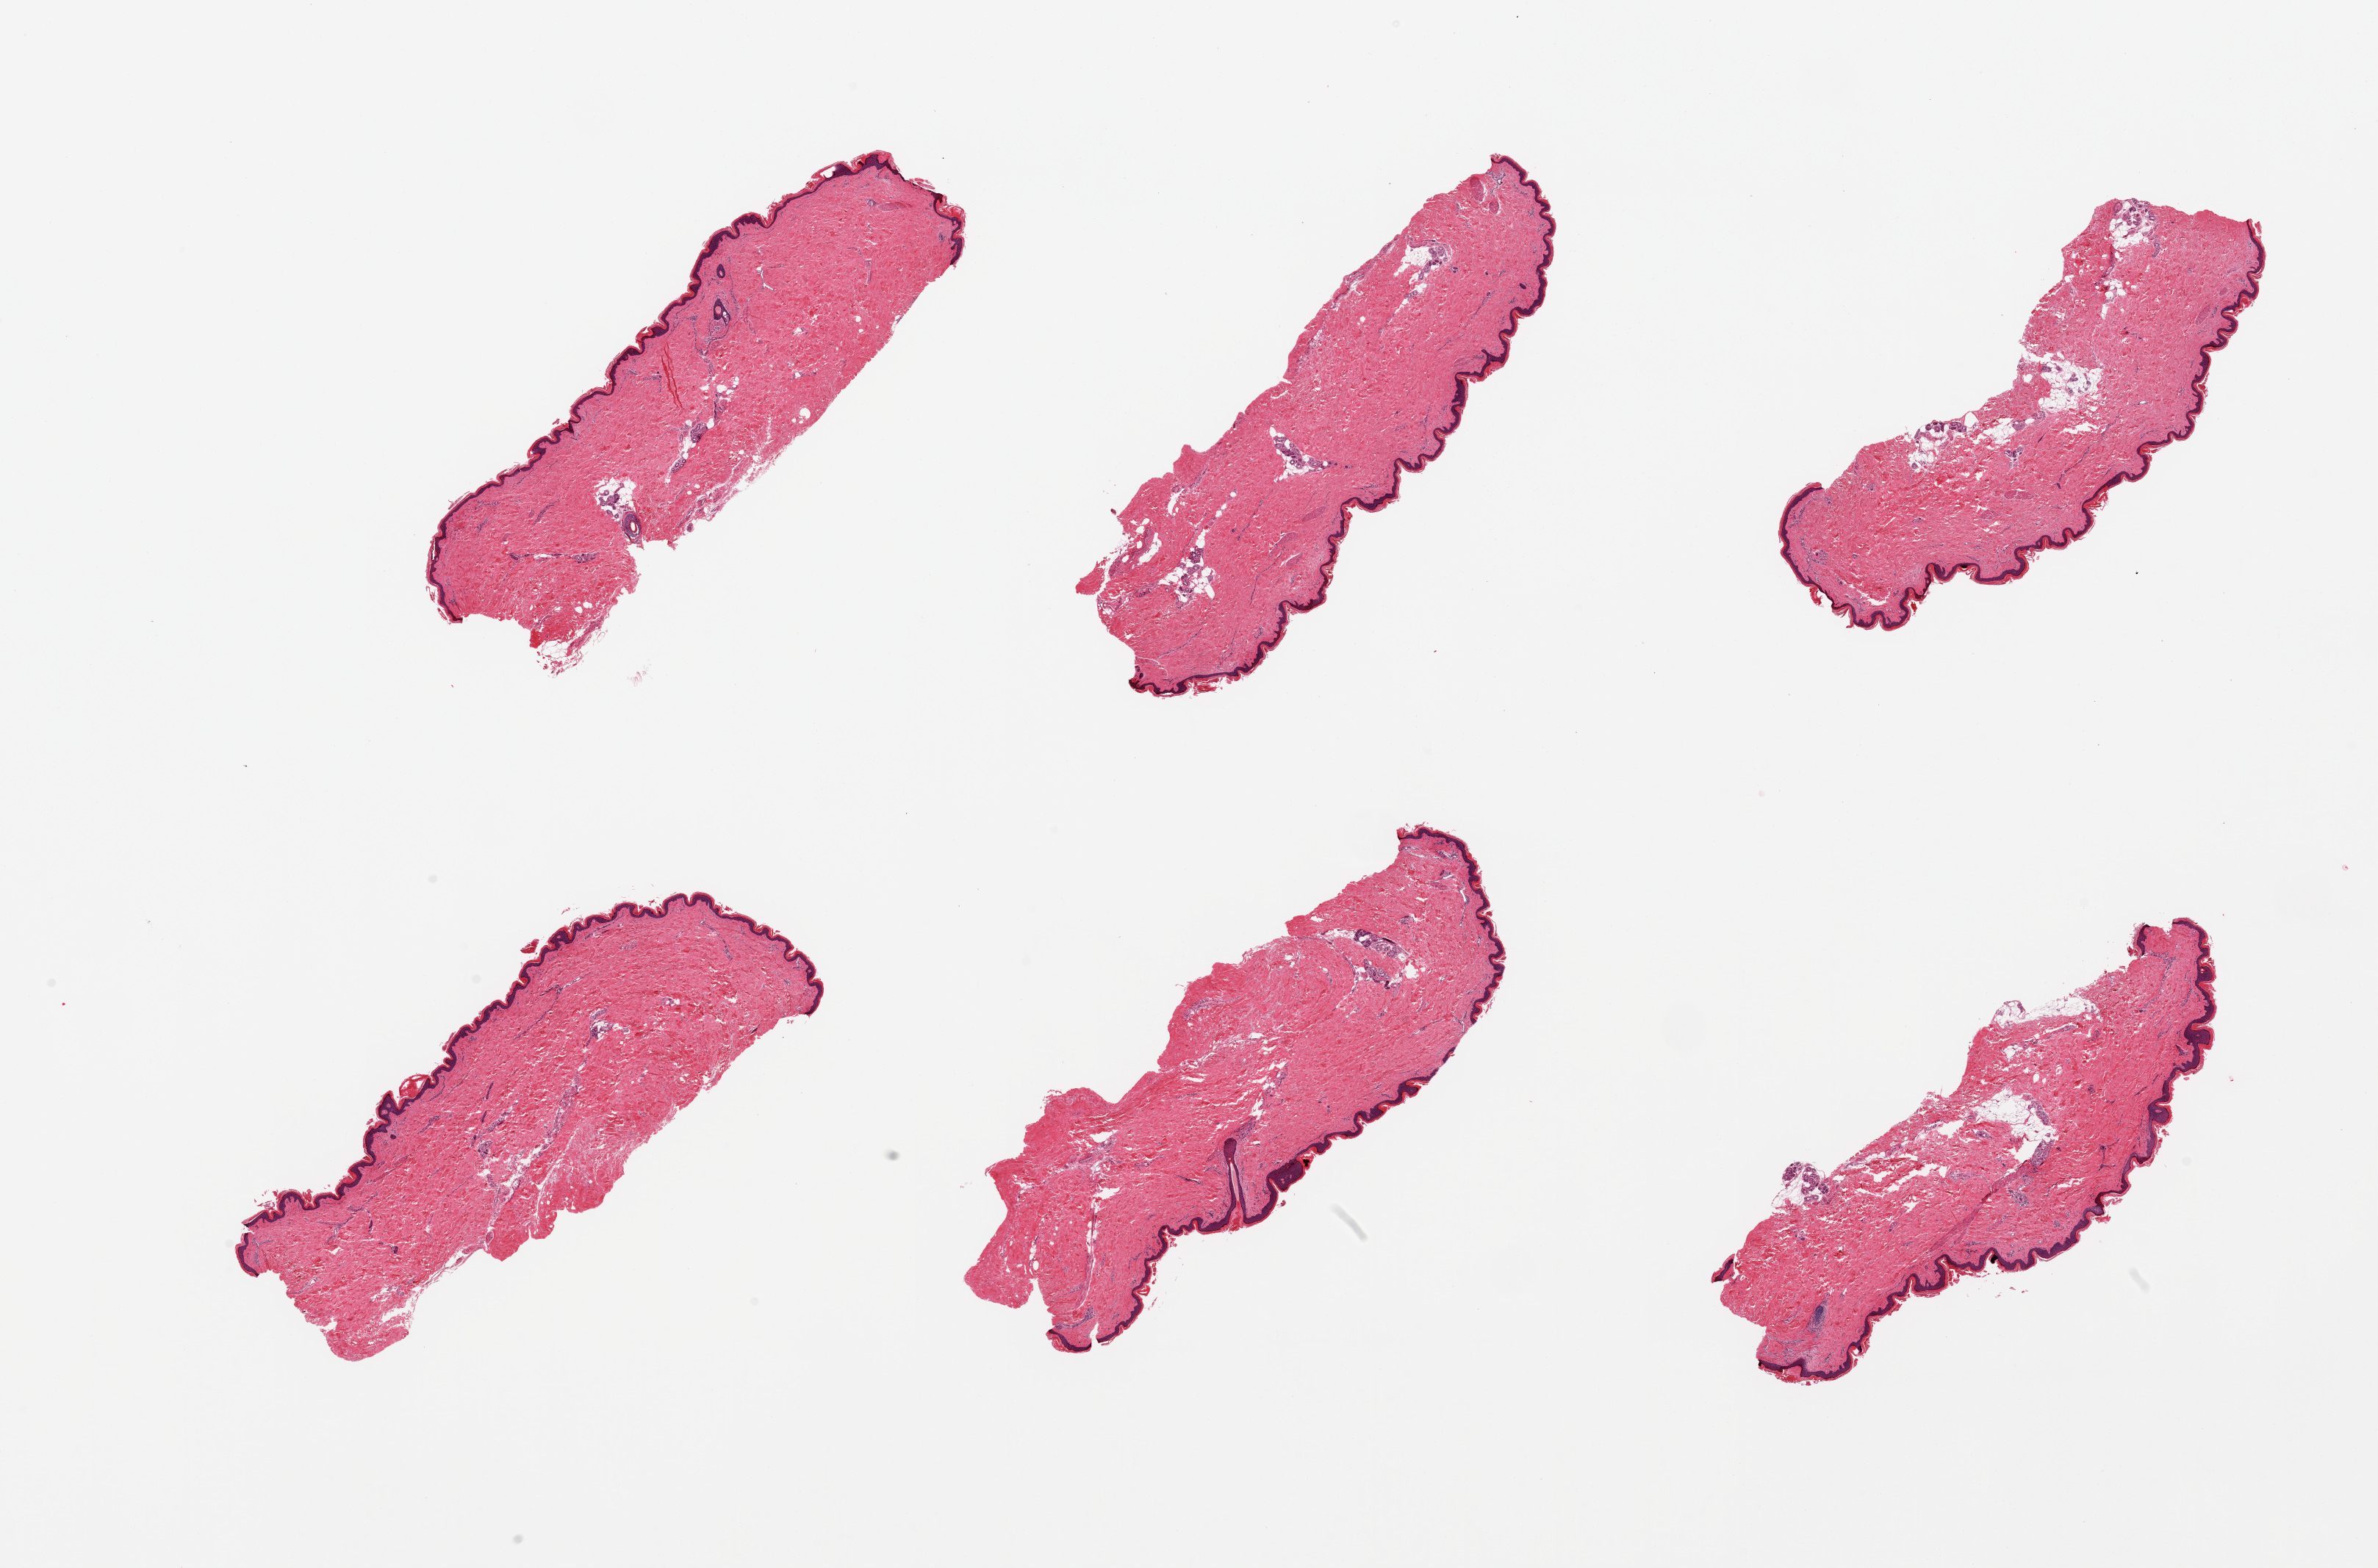
Haematoxylin and eosin whole-slide image — a low-resolution overview of the entire scanned area, about 25.6 x 16.9 mm, PAXgene-fixed, paraffin-embedded tissue, section of skin of lower leg (target tissue), tissue donor sample. Donor: male.
Review note (as recorded): 6 pieces; up to 10% dermal fat.